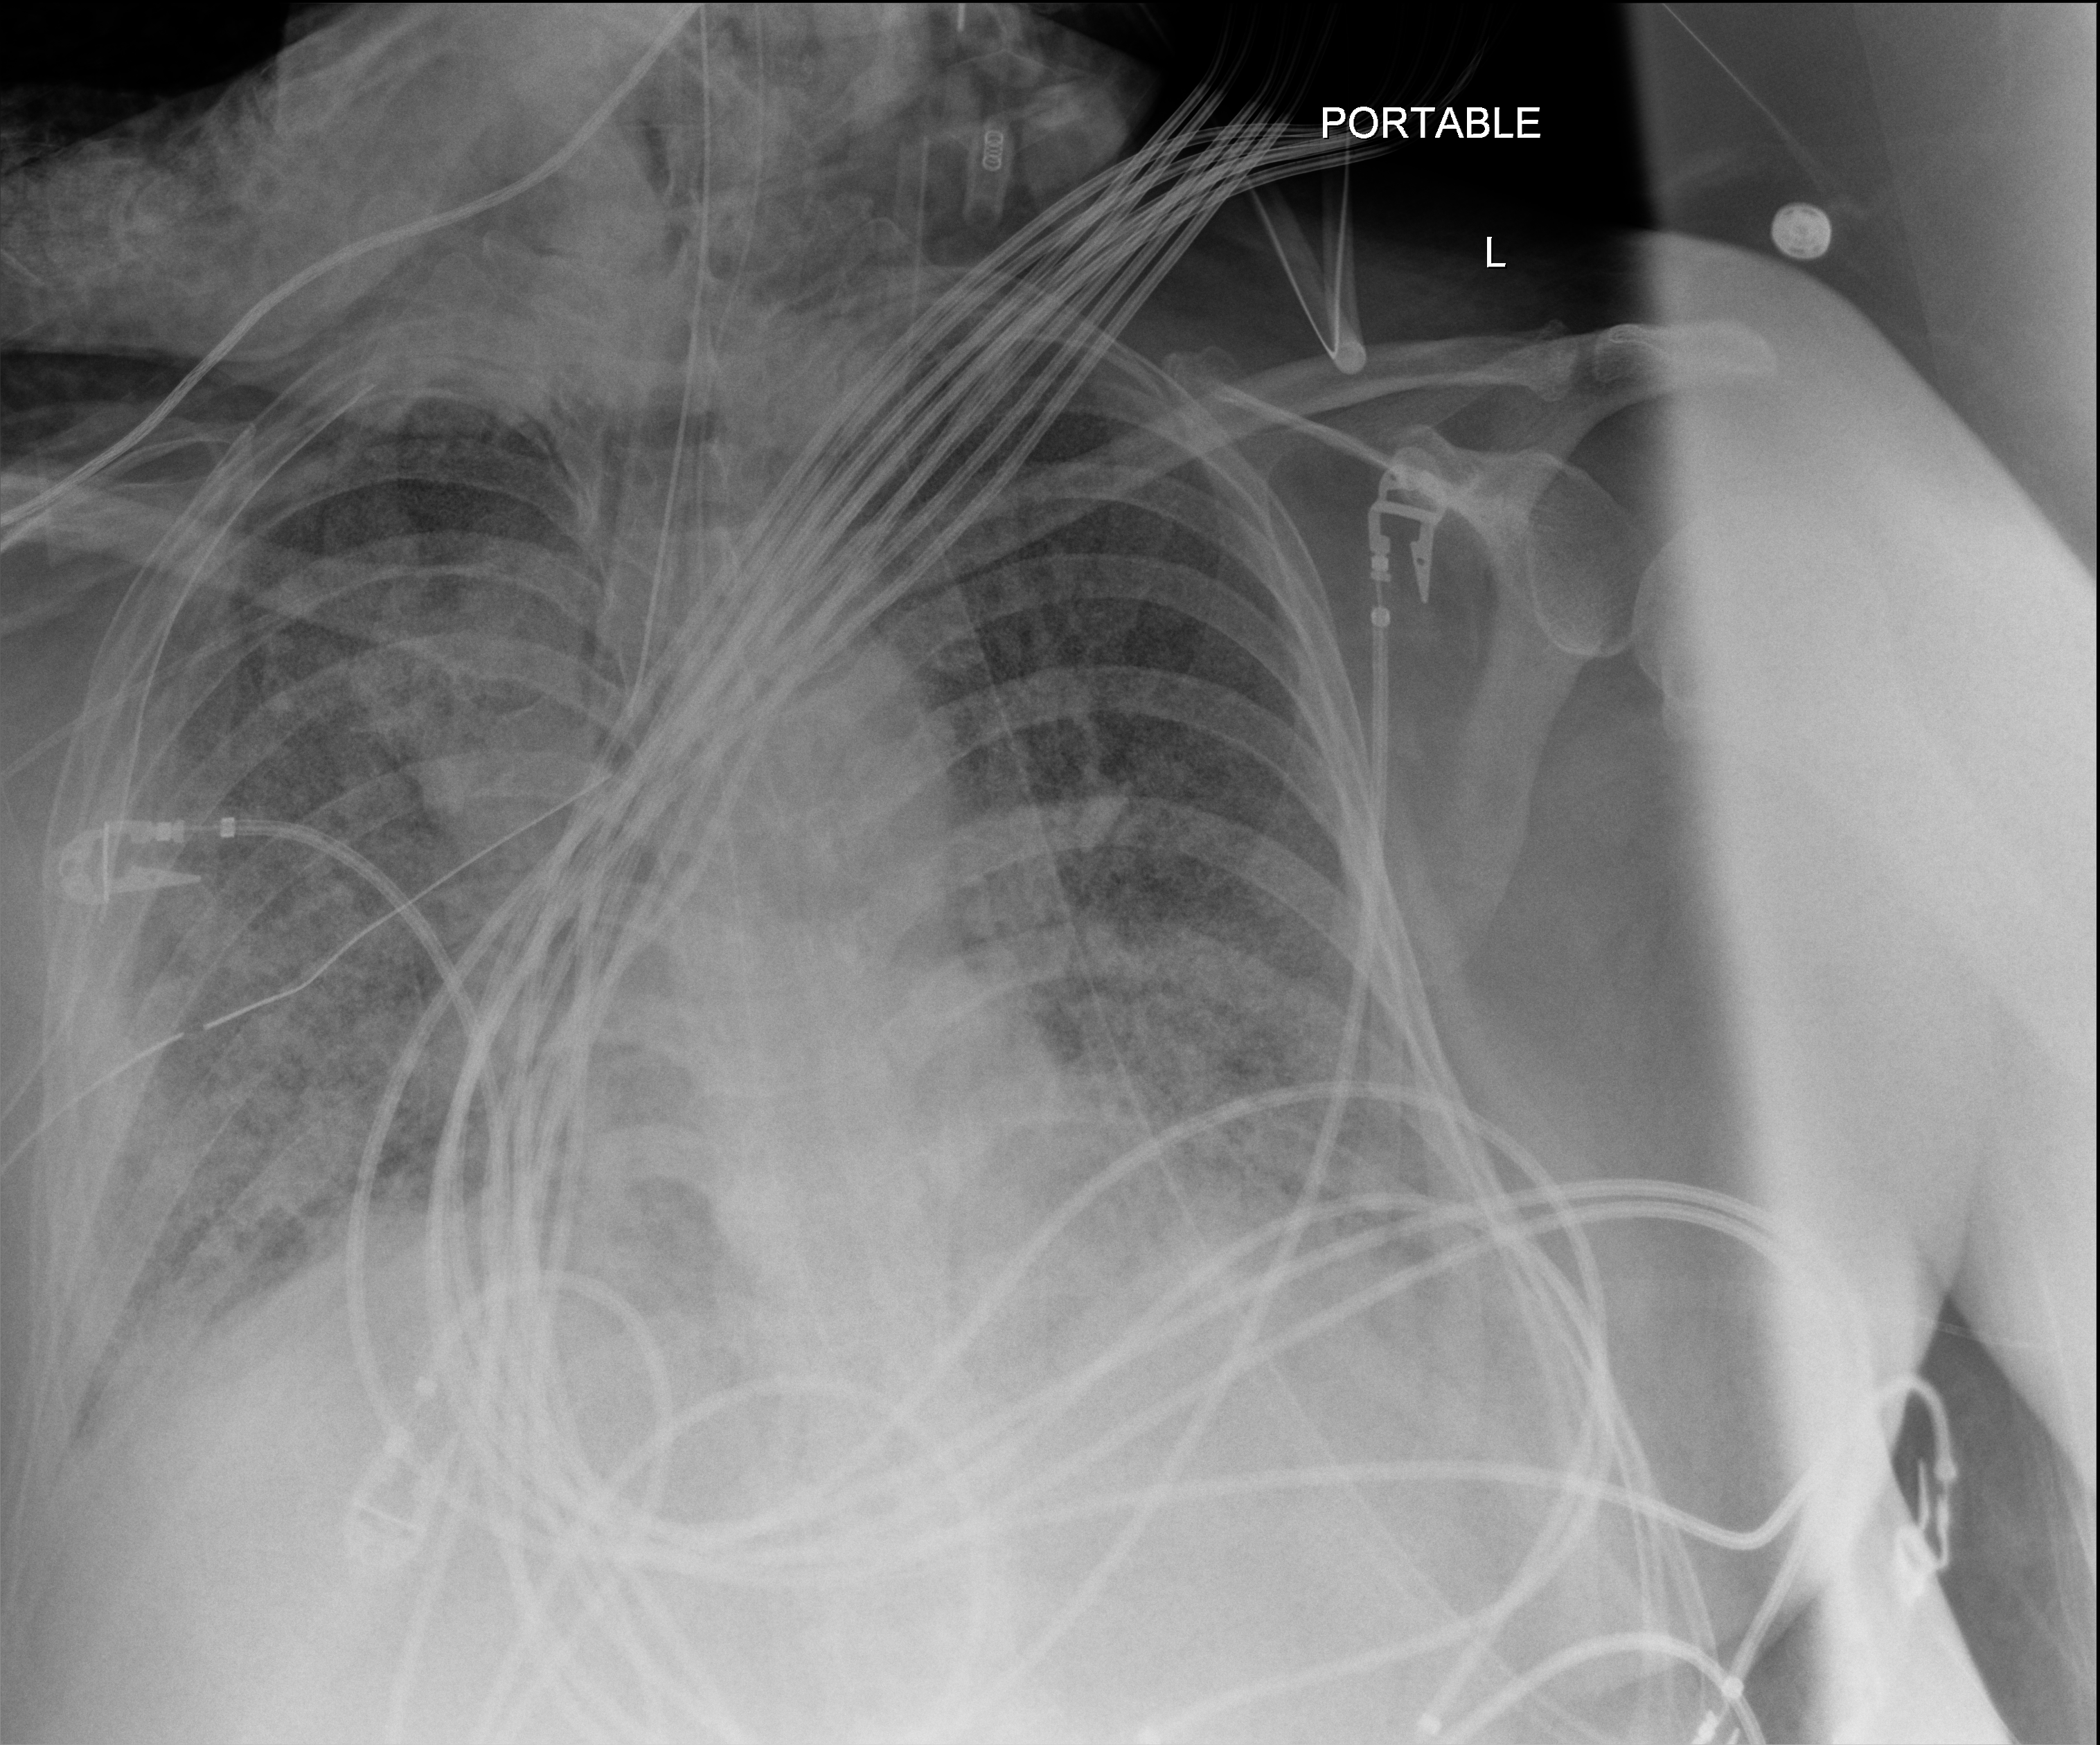
Bedside chest radiograph (digital radiography); anteroposterior (AP) projection. Adult patient hospitalised with COVID-19, age 18–59 years.
From the hospital-stay record, not from the radiograph (when in the stay this image was taken is not recorded): diabetes (admission record): no.